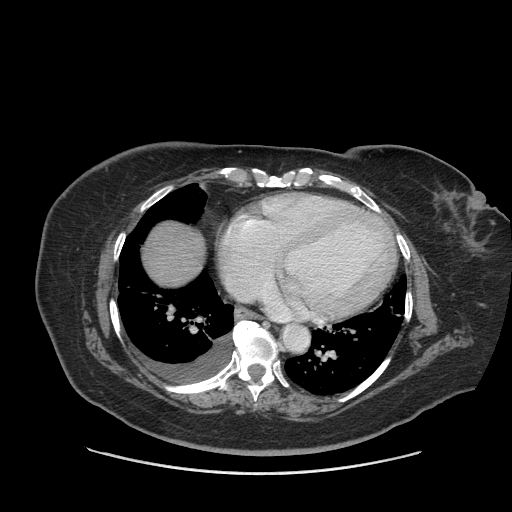
Contrast-enhanced abdominal CT (liver protocol), one axial slice. Position 85 of 91 along the scan axis. Reconstruction kernel STANDARD. 140 kVp. Soft-tissue window (W 400 / L 40 HU). 2.5 mm slice thickness. 512 × 512 image matrix, field of view 420 × 420 mm. Case-level facts recorded for this patient, not image findings: diagnosis: hepatocellular carcinoma (patient treated with transarterial chemoembolisation; whether this scan precedes or follows treatment is not stated here); TNM stage (as recorded): Stage-I; Child-Pugh class: A.
Outlined on this slice (semi-automatic segmentation, software-assisted and operator-edited):
- liver parenchyma outside the tumour (the mass and vessels are separate outlines, so this box may not span the whole liver): box from (x=142, y=220) to (x=204, y=285) px